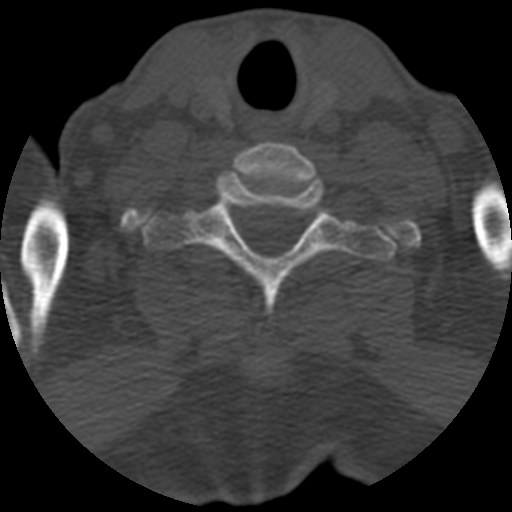
CT including the spine, one axial slice. Position 522 of 708 along the scan axis. 120 kVp. One of 3 acquisitions stored at this slice position. Bone window (W 1800 / L 400 HU). 1.25 mm slice thickness. 512 × 512 image matrix, field of view 160 × 160 mm. Patient age 55 years. From the clinical record (not read from this slice): primary cancer: colon; vertebrae with lytic lesions (as recorded): T12, L1, L5.
Outlined on this slice (semi-automatic segmentation, software-assisted and operator-edited):
- T1 vertebra: bounding box <144,176,394,322> (left, top, right, bottom; pixels)